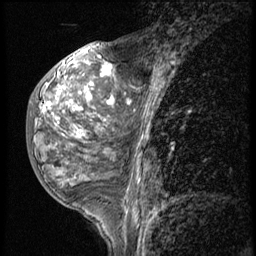
Breast MRI (dynamic contrast-enhanced), one sagittal slice. Slice 21 of 56 in the series (ordered by position). 3 images stored at this slice position (order not interpretable as contrast timing). 1.5 T. TE 4.2 ms, TR 9 ms. 256 × 256 image matrix, field of view 180 × 180 mm. Patient: female, 50 years. From the clinical record (not read from this slice): setting: breast cancer imaged before/during neoadjuvant chemotherapy; receptor status: triple-negative.
Outlined on this slice (semi-automatically segmented with operator editing):
- analysis volume of interest (the breast-tissue region the enhancement analysis was run in; not a lesion): bounding box (x1, y1, x2, y2) in pixels: (26, 50, 117, 191)
- tumour enhancement mask (voxels above the 140 % enhancement threshold inside the analysis volume of interest): (42, 63, 114, 138)